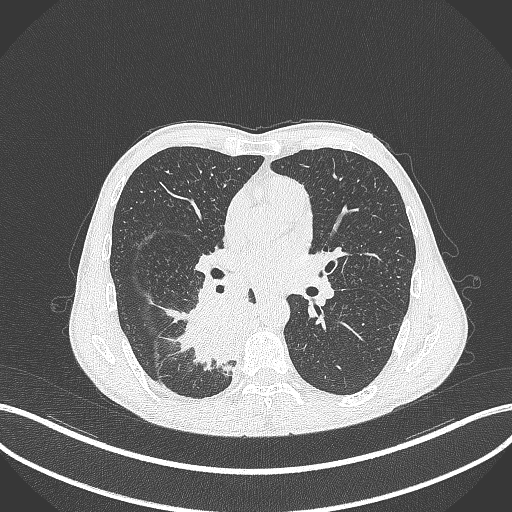
Chest CT, one axial slice. Position 195 of 371 along the scan axis. Lung window (W 1500 / L -600 HU). 512 × 512 image matrix, field of view 400 × 400 mm. Patient: male, 58 years. Case-level facts recorded for this patient, not image findings: clinical TNM (as recorded): T3 N1 M1.
Outlined on this slice (bounding box drawn by a radiologist):
- lung tumour (recorded histology: squamous cell carcinoma): box from (x=155, y=283) to (x=261, y=371) px